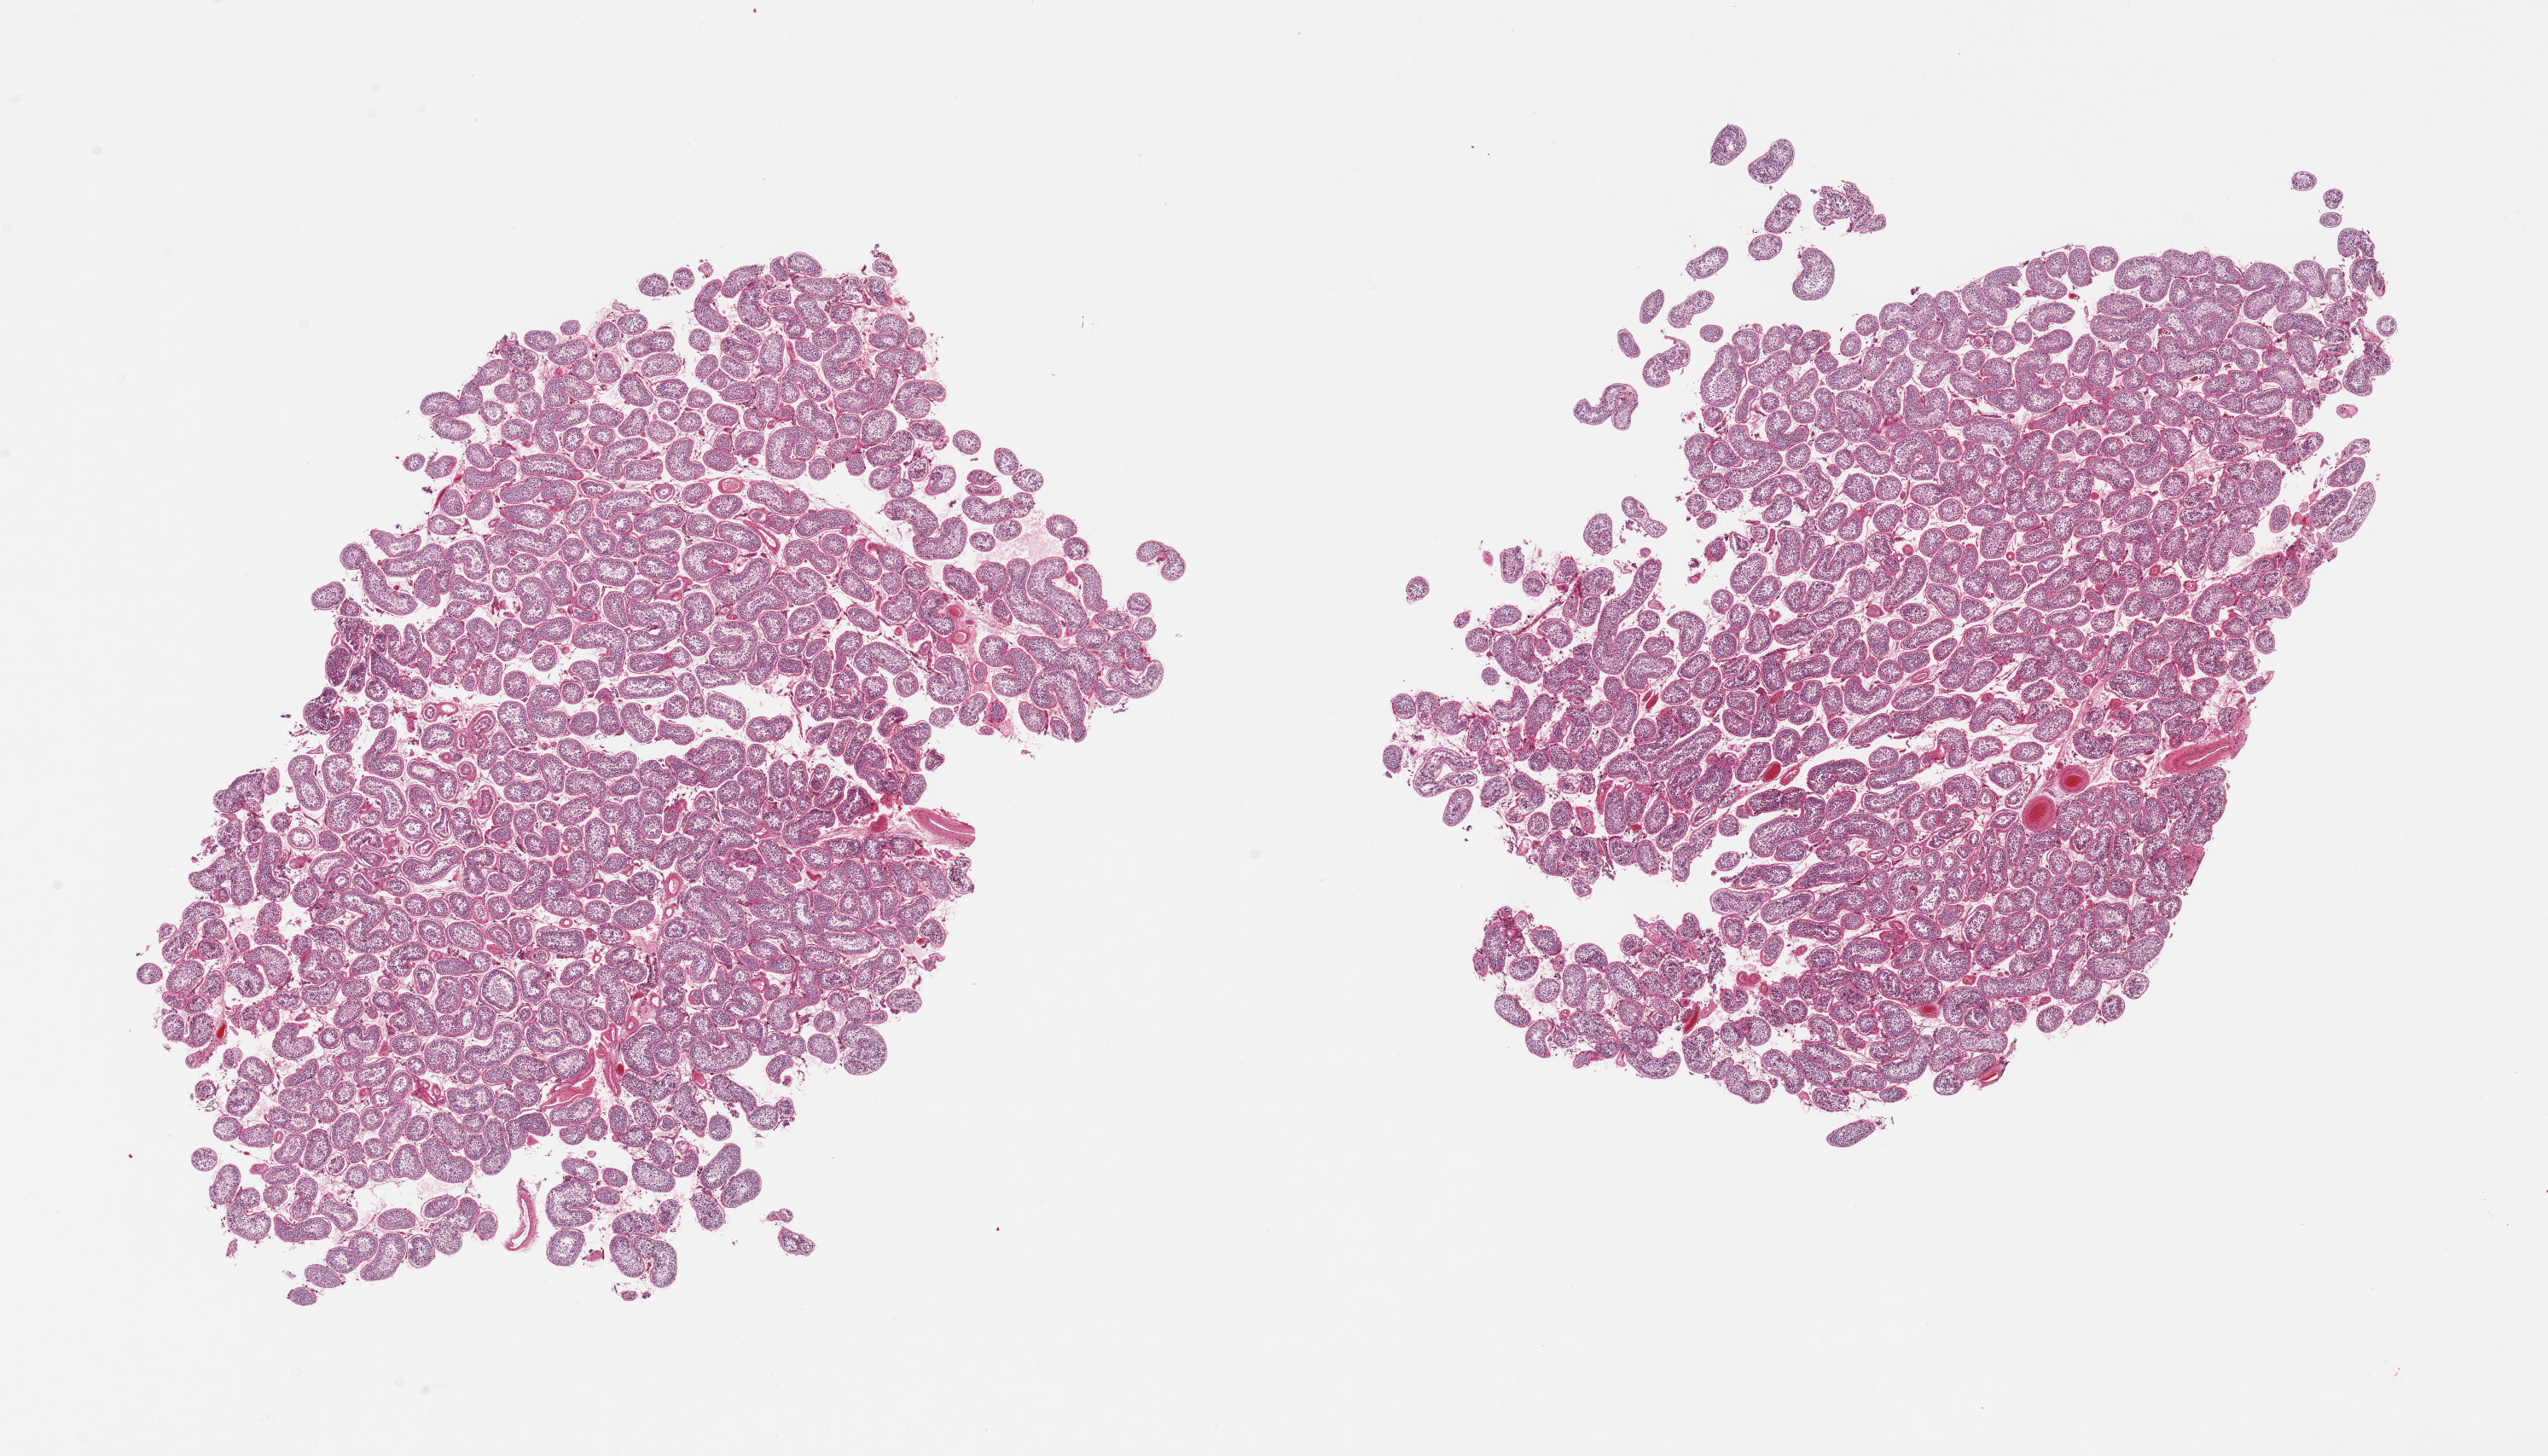
Whole-slide image, H&E stain, a low-resolution overview of the entire scanned area, about 23.6 x 13.5 mm, PAXgene-fixed, paraffin-embedded tissue, sampled site (target tissue): testis, donor tissue sample. Male donor.
* review note (as recorded): 2 pieces; spermatogenesis is present, appears slightly reduced